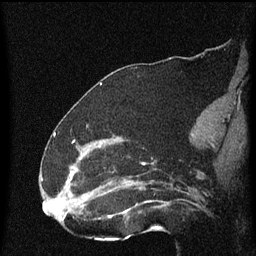
Breast MRI (dynamic contrast-enhanced), one sagittal slice; position 31 of 60 along the scan axis; dynamic contrast-enhanced series, image 2 of 4 at this slice position (ordered by acquisition); 1.5 T; TE 4.2 ms, TR 8 ms; 2 mm slice thickness; 256 × 256 image matrix, field of view 180 × 180 mm. Patient: female, 52 years.
Outlined on this slice (semi-automatically segmented with operator editing):
- analysis volume of interest (the breast-tissue region the enhancement analysis was run in; not a lesion): bounding box <73,148,169,219> (left, top, right, bottom; pixels)
- tumour enhancement mask (voxels above the 70 % enhancement threshold inside the analysis volume of interest): <73,154,152,219>